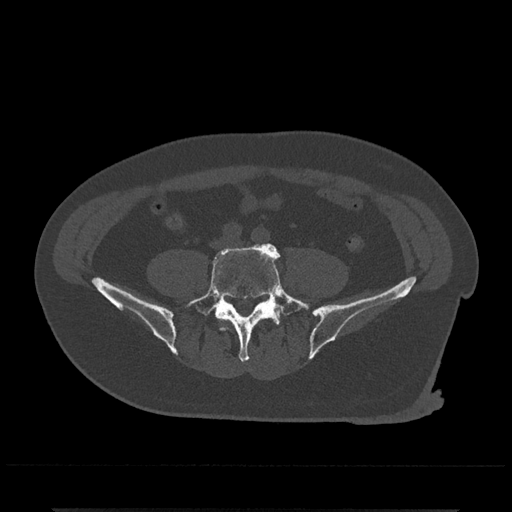
CT including the spine, one axial slice; position 89 of 797 along the scan axis; reconstruction kernel Br40s/3; bone window (W 1800 / L 400 HU); 512 × 512 image matrix, field of view 393 × 393 mm. Male patient, age 67 years. Case-level facts recorded for this patient, not image findings: primary cancer: prostate.
Structures marked on this image (semi-automatic segmentation, software-assisted and operator-edited):
- L4 vertebra: bounding box [x1, y1, x2, y2] px = [222, 328, 226, 330]
- L5 vertebra: [185, 243, 311, 363]